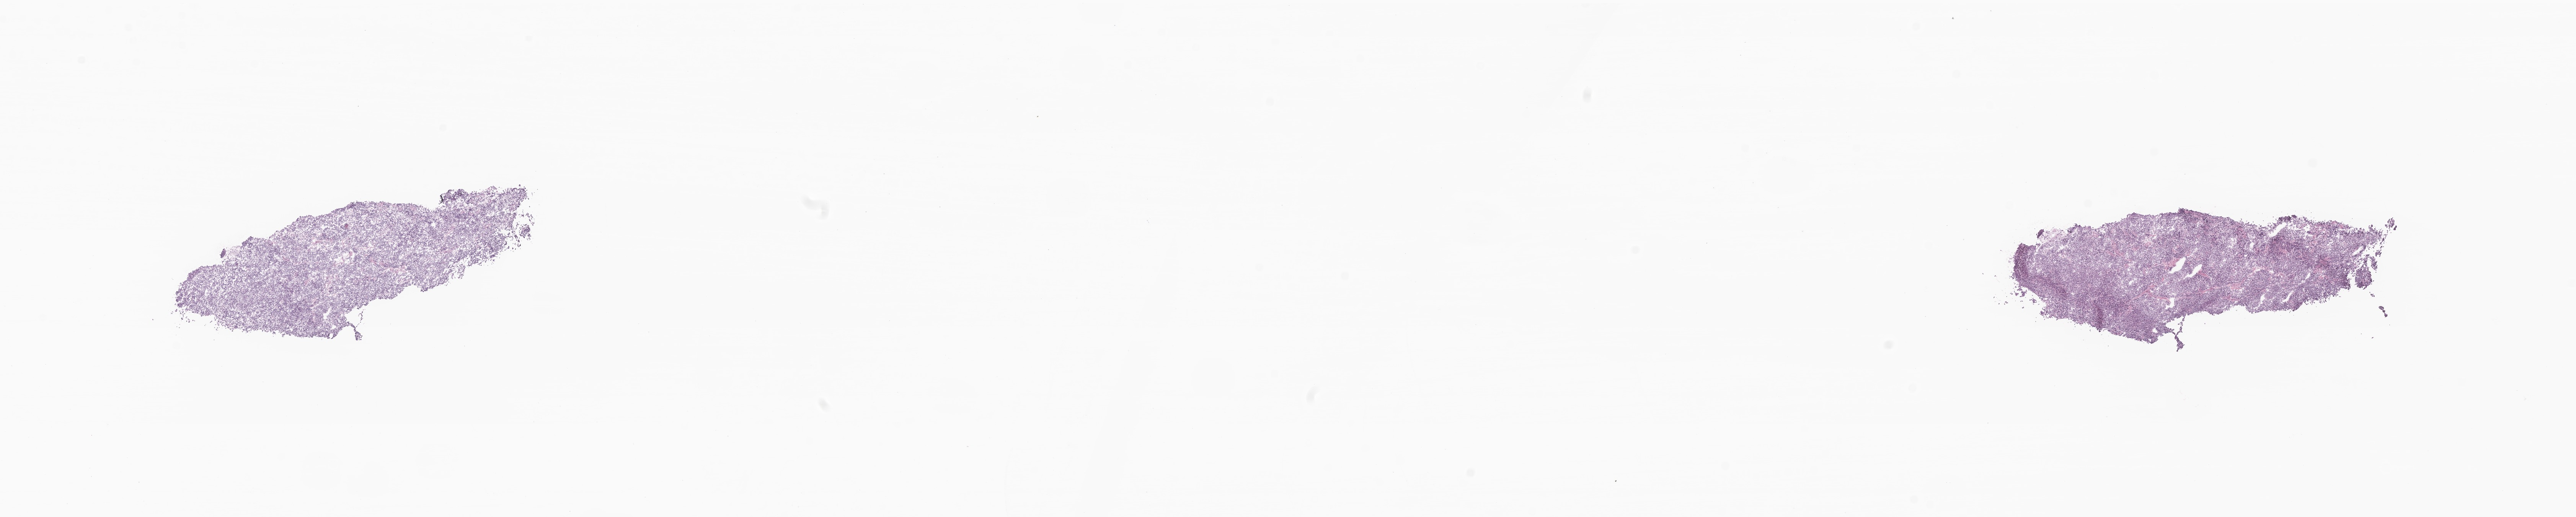
Whole-slide image, H&E stain of tumor tissue from the cerebellum, a low-resolution overview of the entire scanned area, about 28.4 x 5.7 mm; frozen section. Patient: male, age 95 months.
* diagnosis (ICD-O-3 morphology term): Medulloblastoma, NOS